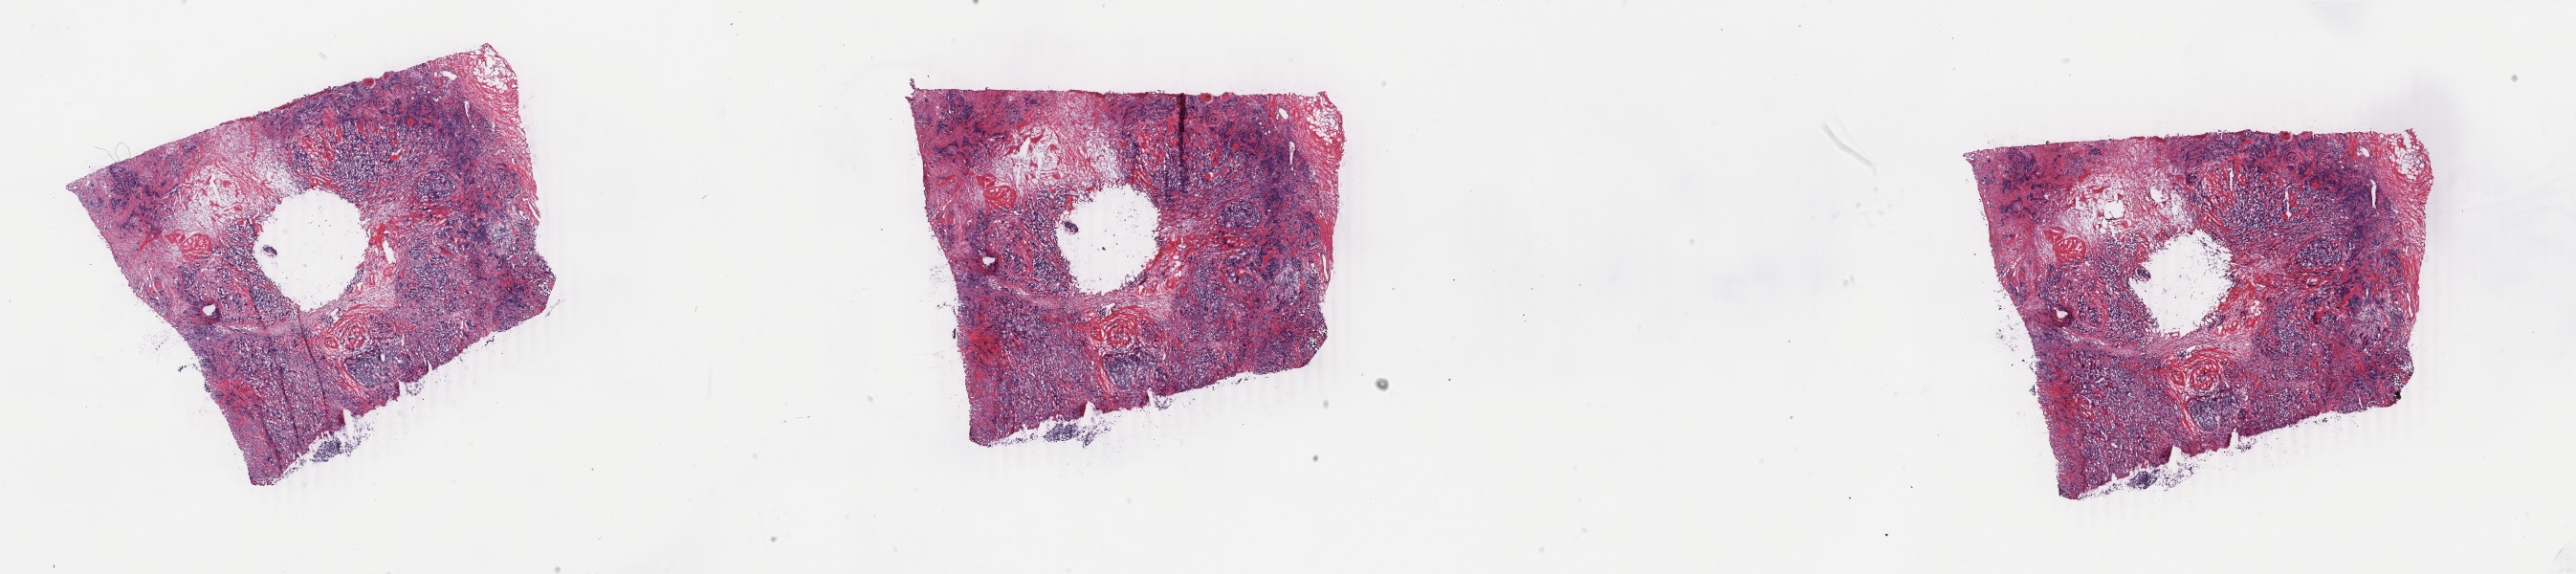
Whole-slide histology image, H&E — a low-resolution overview of the entire scanned area, about 42.8 x 9.5 mm; frozen section; primary tumour sample from the breast. Female patient; age at initial diagnosis 49 years. Composition of this section per pathologist review: tumour cells 80%, tumour nuclei 80%, normal cells 2%, stromal cells 18%, necrosis 0%. Infiltration values recorded for this section: lymphocyte infiltration 2%, monocyte infiltration 0%, neutrophil infiltration 0%.
* diagnosis: Infiltrating duct carcinoma, NOS
* laterality: left
* lymph nodes positive (case pathology): 6 of 32 examined
* AJCC pathologic stage: IIA (3rd edition)